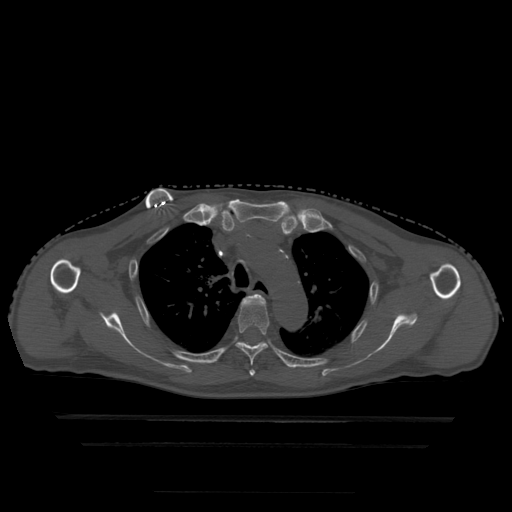
CT including the spine, one axial slice; position 353 of 522 along the scan axis; bone window (W 1800 / L 400 HU); 1.25 mm slice thickness; 512 × 512 image matrix, field of view 436 × 436 mm. Patient age 68 years. Case-level facts recorded for this patient, not image findings: primary cancer: urothelial.
Structures marked on this image (semi-automatic segmentation, software-assisted and operator-edited):
- T3 vertebra: bounding box [x1, y1, x2, y2] px = [244, 294, 265, 374]
- T4 vertebra: [236, 296, 269, 377]
- T5 vertebra: [244, 343, 260, 346]